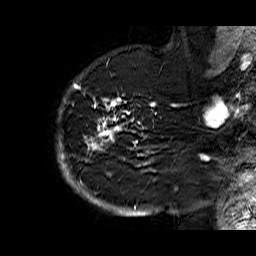
Breast MRI (dynamic contrast-enhanced), one sagittal slice. Slice 50 of 60 in the series (ordered by position). Dynamic contrast-enhanced series, time point 2 of 6 at this slice position (early post-contrast). 1.5 T. TE 6.3 ms, TR 32.9 ms. 4 mm slice thickness. 256 × 256 image matrix, field of view 200 × 200 mm. Female patient. From the clinical record (not read from this slice): setting: breast cancer imaged before/during neoadjuvant chemotherapy; receptor status: HR-positive, HER2-negative.
Annotated regions visible in this slice (semi-automatic segmentation, software-assisted and operator-edited):
- analysis volume of interest (the breast-tissue region the enhancement analysis was run in; not a lesion): bounding box <56,74,176,210> (left, top, right, bottom; pixels)
- tumour enhancement mask (voxels above the 100 % enhancement threshold inside the analysis volume of interest): <57,74,176,210>